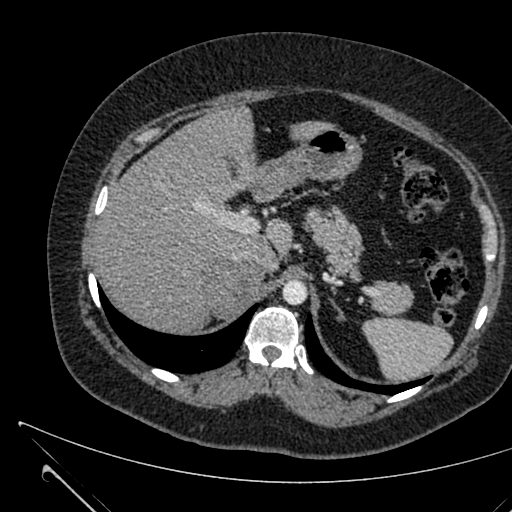
Contrast-enhanced abdominal CT, one axial slice; position 474 of 731 along the scan axis; intravenous contrast given; soft-tissue window (W 400 / L 40 HU); 1 mm slice thickness; 512 × 512 image matrix, field of view 376 × 376 mm. Female patient, age 36 years. From the clinical record (not read from this slice): diagnosis: adrenocortical carcinoma; tumour side: right adrenal; tumour size at pathology: 10 cm; Ki-67 index: 20 %; stage (as recorded): 4.
Structures marked on this image (semi-automatic segmentation, software-assisted and operator-edited):
- mass: bounding box <205,263,263,317> (left, top, right, bottom; pixels)